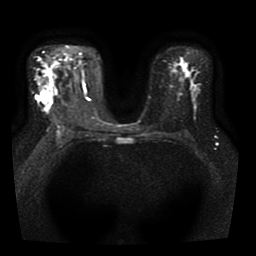
Breast MRI, one axial slice; slice 26 of 41 in the series (ordered by position); diffusion-weighted series; image 2 of 4 stored at this slice position (different b-values; order by instance number); 1.5 T; 256 × 256 image matrix, field of view 330 × 330 mm. Female patient.
Annotated regions visible in this slice (outlined manually by an expert reader):
- tumour on diffusion-weighted imaging: bounding box <37,93,51,103> (left, top, right, bottom; pixels)